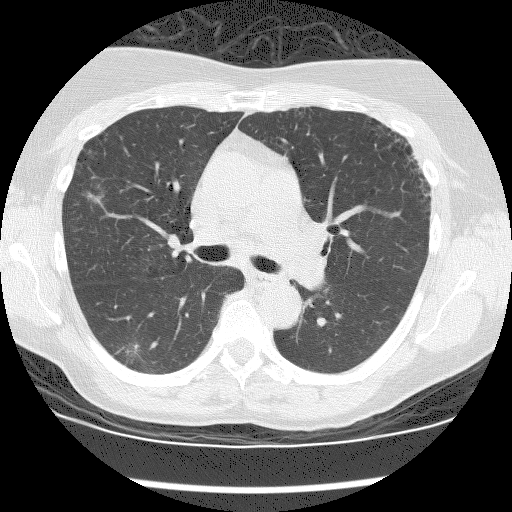
Low-dose screening chest CT, axial slice. First (baseline) screen. Lung window (W 1500 / L -600 HU). Slice 61 of 176 in the series. 512 × 512 image matrix, field of view 320 × 320 mm. Female participant, aged 59 years at enrolment. Current smoker at enrolment.
• Expert-annotated lung lesion, bounding box (x1, y1, x2, y2) in pixels: (109, 339, 149, 373).
• The screening reader recorded 6 non-calcified nodules or masses ≥4 mm on this exam (right upper lobe, right upper lobe, right lower lobe, right lower lobe, right upper lobe, right upper lobe); which of them this box marks is not recorded.
• Official screen result: positive, change unspecified: nodule(s) >= 4 mm or enlarging nodule(s), mass(es), or other non-specific abnormalities suspicious for lung cancer.
• Later outcome: lung cancer diagnosed 242 days after this screen — adenocarcinoma, NOS, right lower lobe, moderately differentiated (G2), stage IIIA (AJCC 6th edition), 12 mm at pathology.